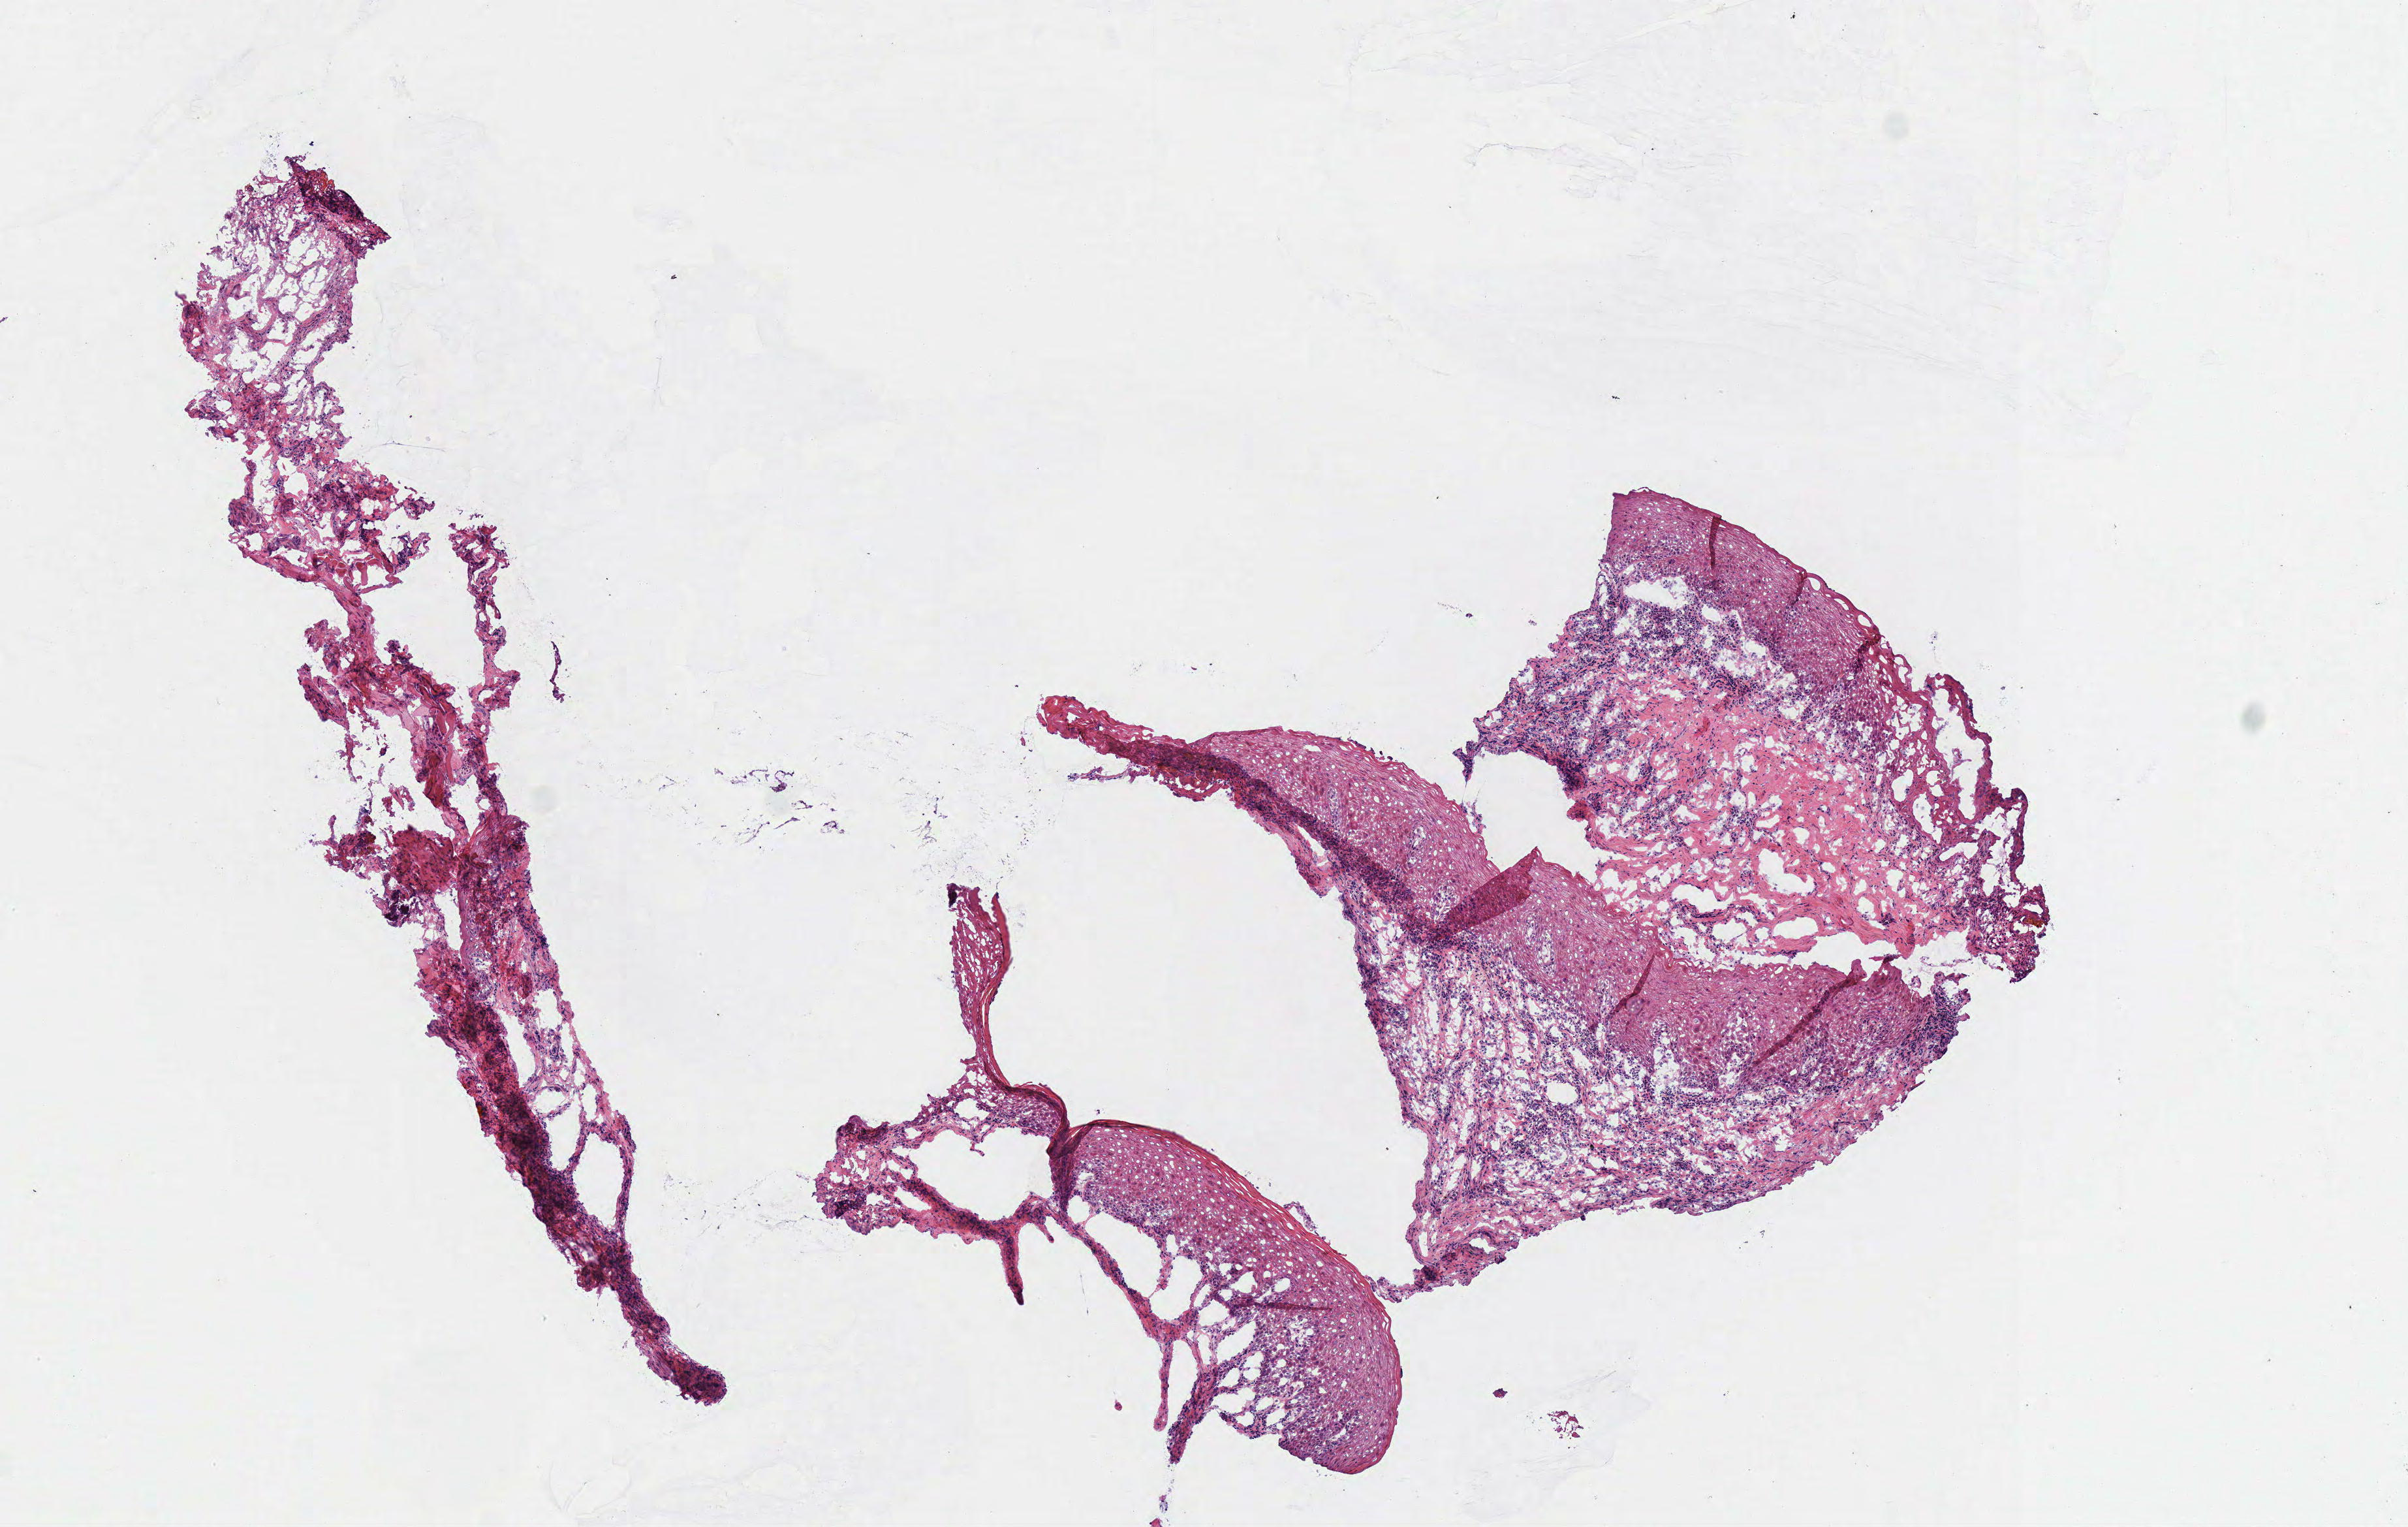
Hematoxylin and eosin (H&E) stained whole-slide image — low-resolution overview of the scanned area, about 7.3 x 4.6 mm, frozen section from the top of the tissue portion, solid tissue normal (non-tumour tissue) sample from the head and neck. Female, age 80 years at initial diagnosis.
• this section: solid tissue normal sample (biorepository sample class)
• patient diagnosis: Squamous cell carcinoma, NOS (floor of mouth, NOS)